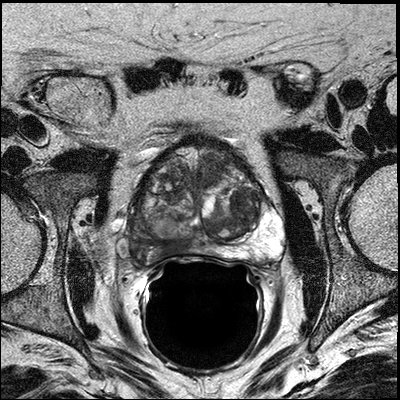
Prostate MRI examination; 3 images, each a single mid-volume slice chosen by position (not for content). Treatment context recorded for this patient: Surgery.
Image 1: T2-weighted axial slice, series "T2W_TSE_AX", slice 19 of 36, 3 mm slice thickness.
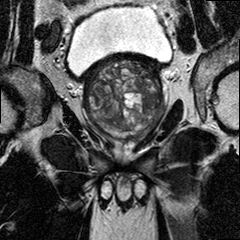
Image 2: coronal T2-weighted image, series "T2W_TSE_COR", slice 16 of 30, 3 mm slice thickness.
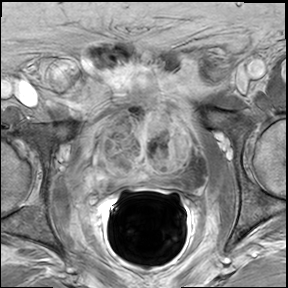
Image 3: axial dynamic contrast-enhanced (DCE) T1-weighted image, slice 19 of 36, dynamic phase 5 of 8.
Report of this MRI examination:
FINDINGS: The prostate has a maximal lateral diameter of 6.3 cm, a maximal craniocaudal diameter of 5.7 cm and a maximal AP diameter of 4.9 cm resulting in an estimated gland volume of 91 cc. The zonal anatomy is preserved. There is a prominent middle lobe due to marked BPH. There is a large suspiciously enhancing tumor seen in the right posterior lateral peripheral zone involving all 3 levels of the prostate from base to apex. Measuring approximately 3.6 x 1.6 x 2.4 cm. At the base the tumor crosses the midline into the left peripheral zone. At the apex and lower midthird, posterior lateral at the 7-8 o'clock position there is capsular infiltration present without manifest tumor mass extending beyond the capsule. (slice location a 33 series 501). There is a large prominent middle lobe present. No evidence for involvement of the neurovascular bundle on either side. No evidence for seminal vesicles infiltration. No evidence of involvement of bladder neck and rectal wall. No suspiciously enlarged obturator and iliac lymph nodes. Multiplanar reconstructions, subtraction images, and CAD analysis of the dynamic series for assessment of the kinetic information facilitated the interpretation of the exam. IMPRESSION: 1) 3.6 cm tumor in the right peripheral zone with capsular infiltration posterior lateral at 7-8 o'clock in the lower mid third and apex, as described above. 2) No evidence of manifest extracapsular decease. 3) No evidence of involvement of the neurovascular bundles on either side, however if nerve sparing is planned, this should be considered only on the left side due to the proximity of the tumor to the right neurovascular bundle and the capsular infiltration on that side. No involvement of the seminal vesicles. No lymphadenopathy. 4) Marked BPH with prominent middle lobe; Prostate volume estimated 91 cc

Biopsy pathology report for this patient (as recorded):
A. PROSTATE, LEFT APEX: BENIGN PROSTATIC TISSUE. NO TUMOR IDENTIFIED. B. PROSTATE, LEFT APEX LATERAL: BENIGN PROSTATIC TISSUE. NO TUMOR IDENTIFIED. C. PROSTATE, RIGHT APEX: PROSTATIC ADENOCARCINOMA, GLEASON GRADE 3+3 = 6/10, INVOLVING 50% OF THE TISSUE, 1 OF 1 CORE. D. PROSTATE, RIGHT APEX LATERAL: PROSTATIC ADENOCARCINOMA, GLEASON GRADE 3+3 = 6/10, INVOLVING 50% OF THE TISSUE, 1 OF 1 CORE. E. PROSTATE, LEFT MID: BENIGN PROSTATIC TISSUE. NO TUMOR IDENTIFIED. F. PROSTATE, LEFT MID LATERAL: BENIGN PROSTATIC TISSUE. NO TUMOR IDENTIFIED. G. PROSTATE, RIGHT MID: BENIGN PROSTATIC TISSUE. NO TUMOR IDENTIFIED. H. PROSTATE, RIGHT MID LATERAL: PROSTATIC TISSUE WITH FOCAL HIGH GRADE PROSTATIC INTRAEPITHELIAL NEOPLASIA (PIN). I. PROSTATE, LEFT BASE: BENIGN PROSTATIC TISSUE. NO TUMOR IDENTIFIED. J. PROSTATE, LEFT BASE LATERAL: PROSTATIC ADENOCARCINOMA, GLEASON GRADE 4+3 = 7/10, INVOLVING 15% OF THE TISSUE, 1 OF 1 CORE. K. PROSTATE, RIGHT BASE: BENIGN PROSTATIC TISSUE. NO TUMOR IDENTIFIED. L. PROSTATE, RIGHT BASE LATERAL: BENIGN PROSTATIC TISSUE. NO TUMOR IDENTIFIED